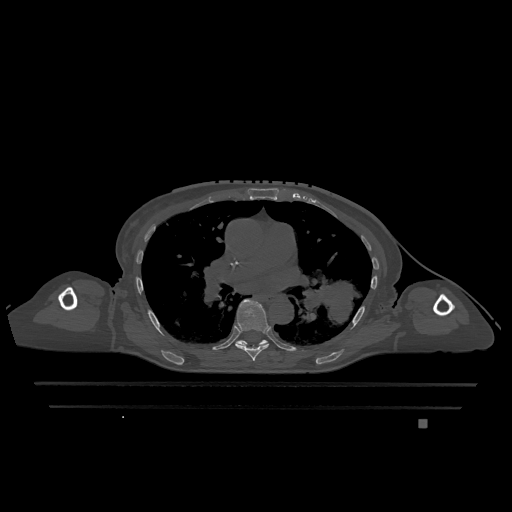
CT including the spine, one axial slice. Position 773 of 1317 along the scan axis. Bone window (W 1800 / L 400 HU). 0.5 mm slice thickness. 512 × 512 image matrix, field of view 500 × 500 mm. Patient: female, 74 years. Case-level facts recorded for this patient, not image findings: primary cancer: lung.
Outlined on this slice (semi-automatically segmented with operator editing):
- T6 vertebra: bounding box [x1, y1, x2, y2] px = [235, 299, 270, 361]
- T7 vertebra: [236, 340, 268, 345]